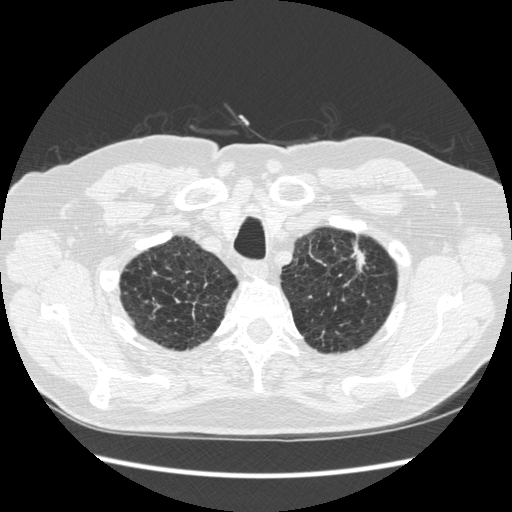
Low-dose screening chest CT, one axial slice; slice 237 of 267 in the series (ordered by position); reconstruction kernel STANDARD; 120 kVp; lung window (W 1500 / L -600 HU); 1.25 mm slice thickness; 512 × 512 image matrix, field of view 360 × 360 mm.
Structures marked on this image (outlined manually by an expert reader):
- lesion 1 (tumor, upper lobe of left lung): bounding box <351,243,365,272> (left, top, right, bottom; pixels)